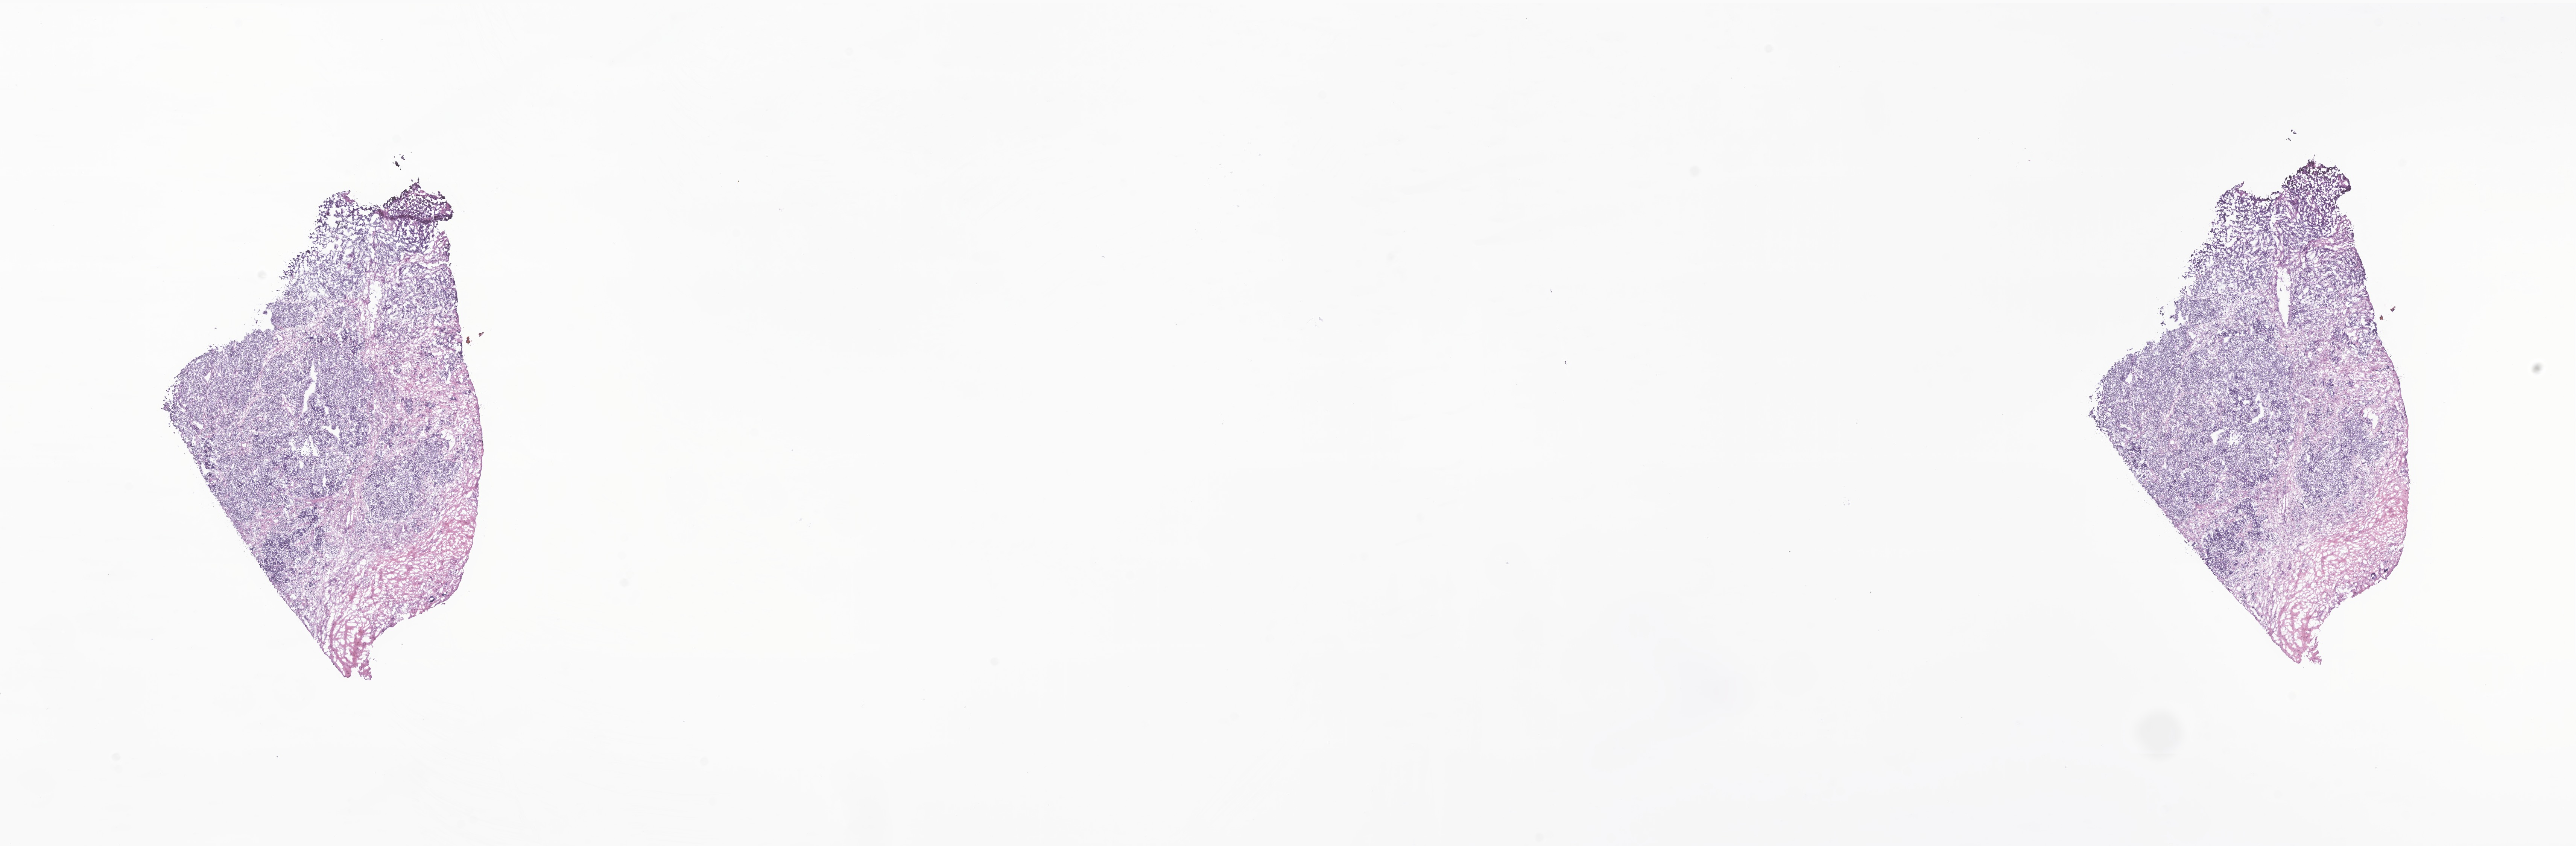
Whole-slide image, haematoxylin and eosin stain of tumor tissue from the retroperitoneum, low-resolution overview of the scanned area, about 28.9 x 9.5 mm. Cryosection (OCT / tissue freezing medium). Patient male; age 811 days (about 2.2 years).
• diagnosis (ICD-O-3 morphology term): Neuroblastoma, NOS